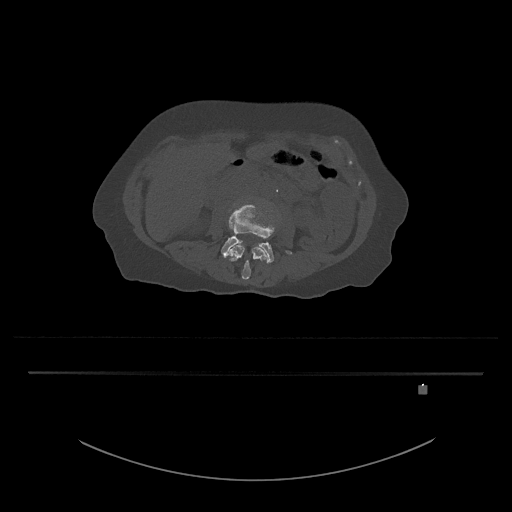
CT including the spine, one axial slice. Slice 393 of 797 in the series (ordered by position). Reconstruction kernel Br40s/3. 120 kVp. Bone window (W 1800 / L 400 HU). 512 × 512 image matrix, field of view 500 × 500 mm. Female patient, age 57 years. From the clinical record (not read from this slice): primary cancer: cervical.
Structures marked on this image (semi-automatically segmented with operator editing):
- L3 vertebra: bounding box (x1, y1, x2, y2) in pixels: (226, 243, 268, 280)
- L4 vertebra: (221, 204, 292, 264)